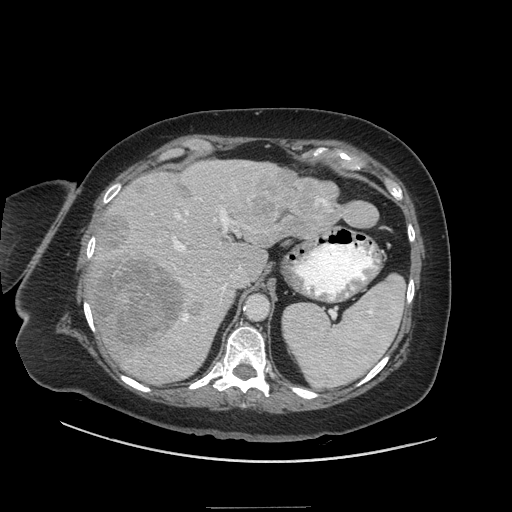
Contrast-enhanced abdominal CT (liver protocol), one axial slice; slice 37 of 81 in the series (ordered by position); reconstruction kernel STANDARD; 140 kVp; soft-tissue window (W 400 / L 40 HU); 512 × 512 image matrix, field of view 440 × 440 mm. From the clinical record (not read from this slice): diagnosis: hepatocellular carcinoma (patient treated with transarterial chemoembolisation; whether this scan precedes or follows treatment is not stated here); TNM stage (as recorded): Stage-II; Child-Pugh class: A; tumour differentiation: moderately differentiated; tumour nodularity: multinodular.
Outlined on this slice (semi-automatic segmentation, software-assisted and operator-edited):
- liver parenchyma outside the tumour (the mass and vessels are separate outlines, so this box may not span the whole liver): bounding box [x1, y1, x2, y2] px = [88, 160, 343, 384]
- mass: [92, 172, 379, 345]
- liver vessels: [151, 164, 249, 331]